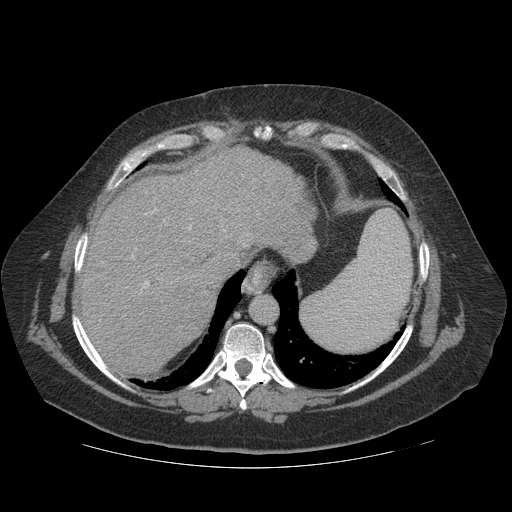
Contrast-enhanced abdominal CT (liver protocol), one axial slice; slice 95 of 121 in the series (ordered by position); soft-tissue window (W 400 / L 40 HU); 512 × 512 image matrix, field of view 420 × 420 mm. Case-level facts recorded for this patient, not image findings: diagnosis: hepatocellular carcinoma (patient treated with transarterial chemoembolisation; whether this scan precedes or follows treatment is not stated here); TNM stage (as recorded): Stage-IIIA; Child-Pugh class: A; tumour differentiation: well differentiated; tumour nodularity: multinodular.
Outlined on this slice (semi-automatic segmentation, software-assisted and operator-edited):
- abdominal aorta: bounding box (x1, y1, x2, y2) in pixels: (251, 297, 277, 324)
- liver parenchyma outside the tumour (the mass and vessels are separate outlines, so this box may not span the whole liver): (76, 146, 316, 374)
- mass: (164, 284, 214, 334)
- liver vessels: (131, 208, 249, 289)